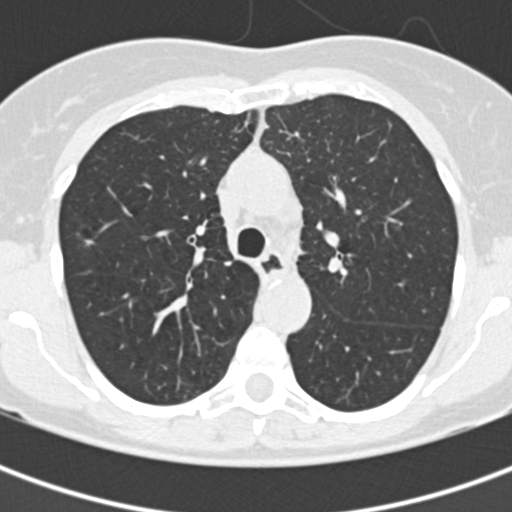
Low-dose screening chest CT, axial slice. First (baseline) screen. Lung window (W 1500 / L -600 HU). 120 kVp. Slice 62 of 177 in the series. 512 × 512 image matrix. Female participant, aged 60 years at enrolment.
Expert-annotated lung lesion, bounding box [x1, y1, x2, y2] px = [62, 221, 110, 269]. No non-calcified nodule or mass ≥4 mm was recorded by the screening reader at this exam. Later outcome: lung cancer diagnosed 861 days after this screen — bronchiolo-alveolar adenocarcinoma, NOS, right upper lobe, well differentiated (G1), stage IA (AJCC 6th edition), 11 mm at pathology.